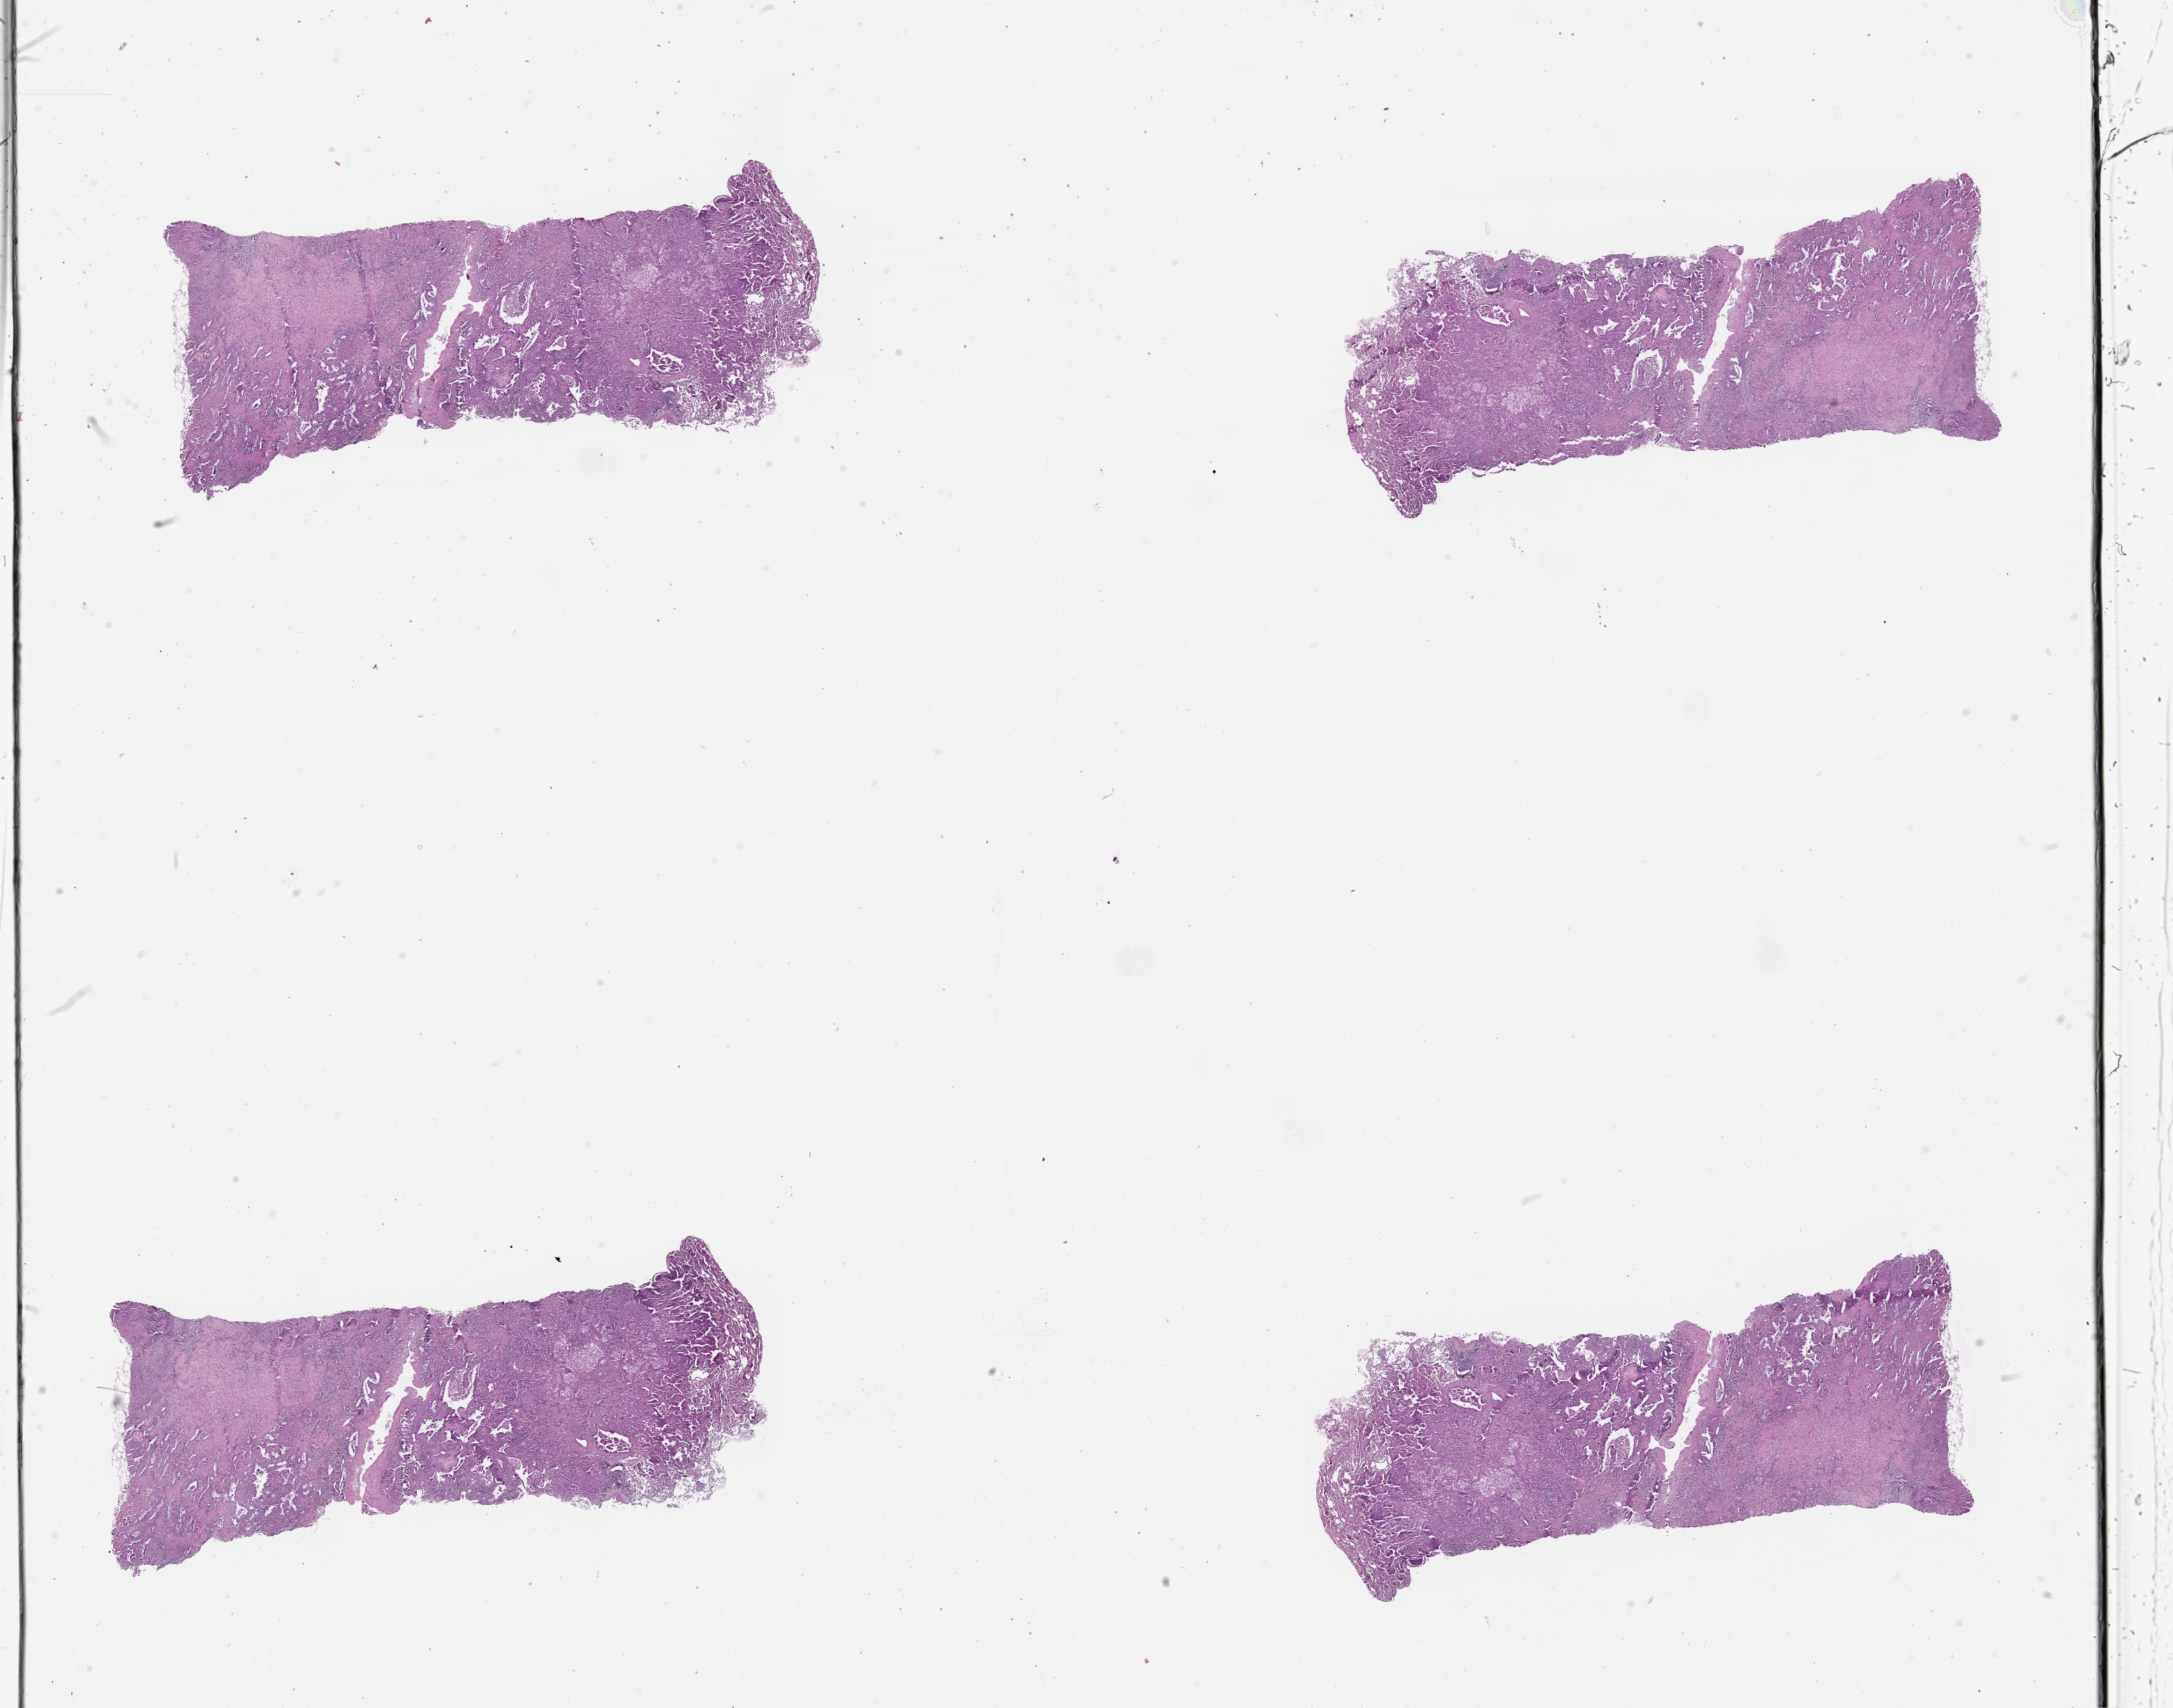
H&E whole-slide image, shown as a low-resolution overview of the whole scanned area (about 25.1 x 19.7 mm, from a 20x scan); tumour tissue sample, sampled site: lung. 51-year-old female patient. Histologic grade: GX (grade cannot be assessed). Composition of this section per pathologist review: tumour nuclei 65%, necrosis 5%.
Histologic diagnosis: Adenocarcinoma, NOS. AJCC pathologic stage: IA. Primary tumour site (as recorded): left lower lobe.